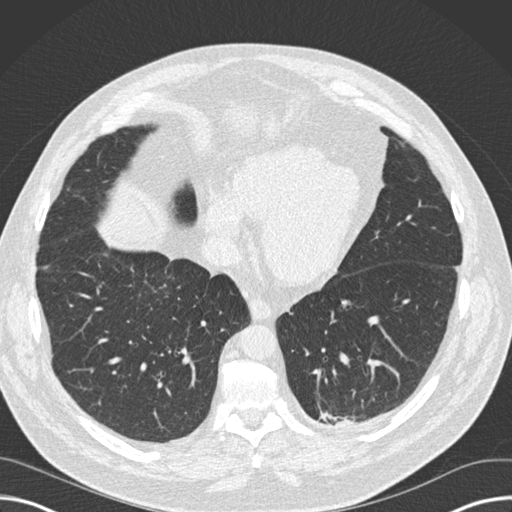
Low-dose screening chest CT, one axial slice; slice 52 of 160 in the series (ordered by position); reconstruction kernel B30f; 120 kVp; lung window (W 1500 / L -600 HU); 512 × 512 image matrix.
Annotated regions visible in this slice (expert manual segmentation):
- lesion 1 (tumor, upper lobe of left lung): bounding box (x1, y1, x2, y2) in pixels: (321, 413, 348, 424)